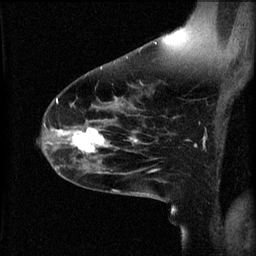
Breast MRI (dynamic contrast-enhanced), one sagittal slice; slice 36 of 60 in the series (ordered by position); 3 images stored at this slice position (order not interpretable as contrast timing); 1.5 T; TE 4.2 ms, TR 8.2 ms; 256 × 256 image matrix, field of view 200 × 200 mm. Female patient, age 49 years.
Structures marked on this image (semi-automatic segmentation, software-assisted and operator-edited):
- analysis volume of interest (the breast-tissue region the enhancement analysis was run in; not a lesion): bounding box <66,124,113,159> (left, top, right, bottom; pixels)
- tumour enhancement mask (voxels above the 70 % enhancement threshold inside the analysis volume of interest): <66,128,109,153>